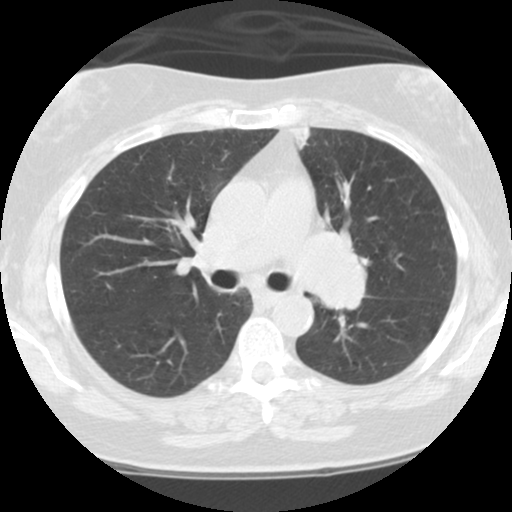
Low-dose screening chest CT, one axial slice. Slice 68 of 108 in the series (ordered by position). Reconstruction kernel STANDARD. 120 kVp. Lung window (W 1500 / L -600 HU). 2.5 mm slice thickness. 512 × 512 image matrix, field of view 300 × 300 mm.
Outlined on this slice (outlined manually by an expert reader):
- lesion 1 (tumor, hilum of left lung): bounding box (x1, y1, x2, y2) in pixels: (297, 234, 368, 318)